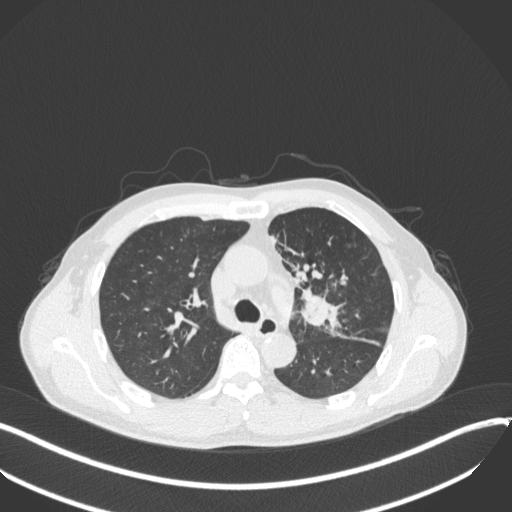
Chest CT, one axial slice; position 230 of 411 along the scan axis; reconstruction kernel B31f; 120 kVp; lung window (W 1500 / L -600 HU); 1 mm slice thickness; 512 × 512 image matrix. Patient: male, 56 years. From the clinical record (not read from this slice): clinical TNM (as recorded): T2a N0 M0.
Structures marked on this image (bounding box drawn by a radiologist):
- lung tumour (recorded histology: squamous cell carcinoma): bounding box [x1, y1, x2, y2] px = [298, 278, 344, 334]